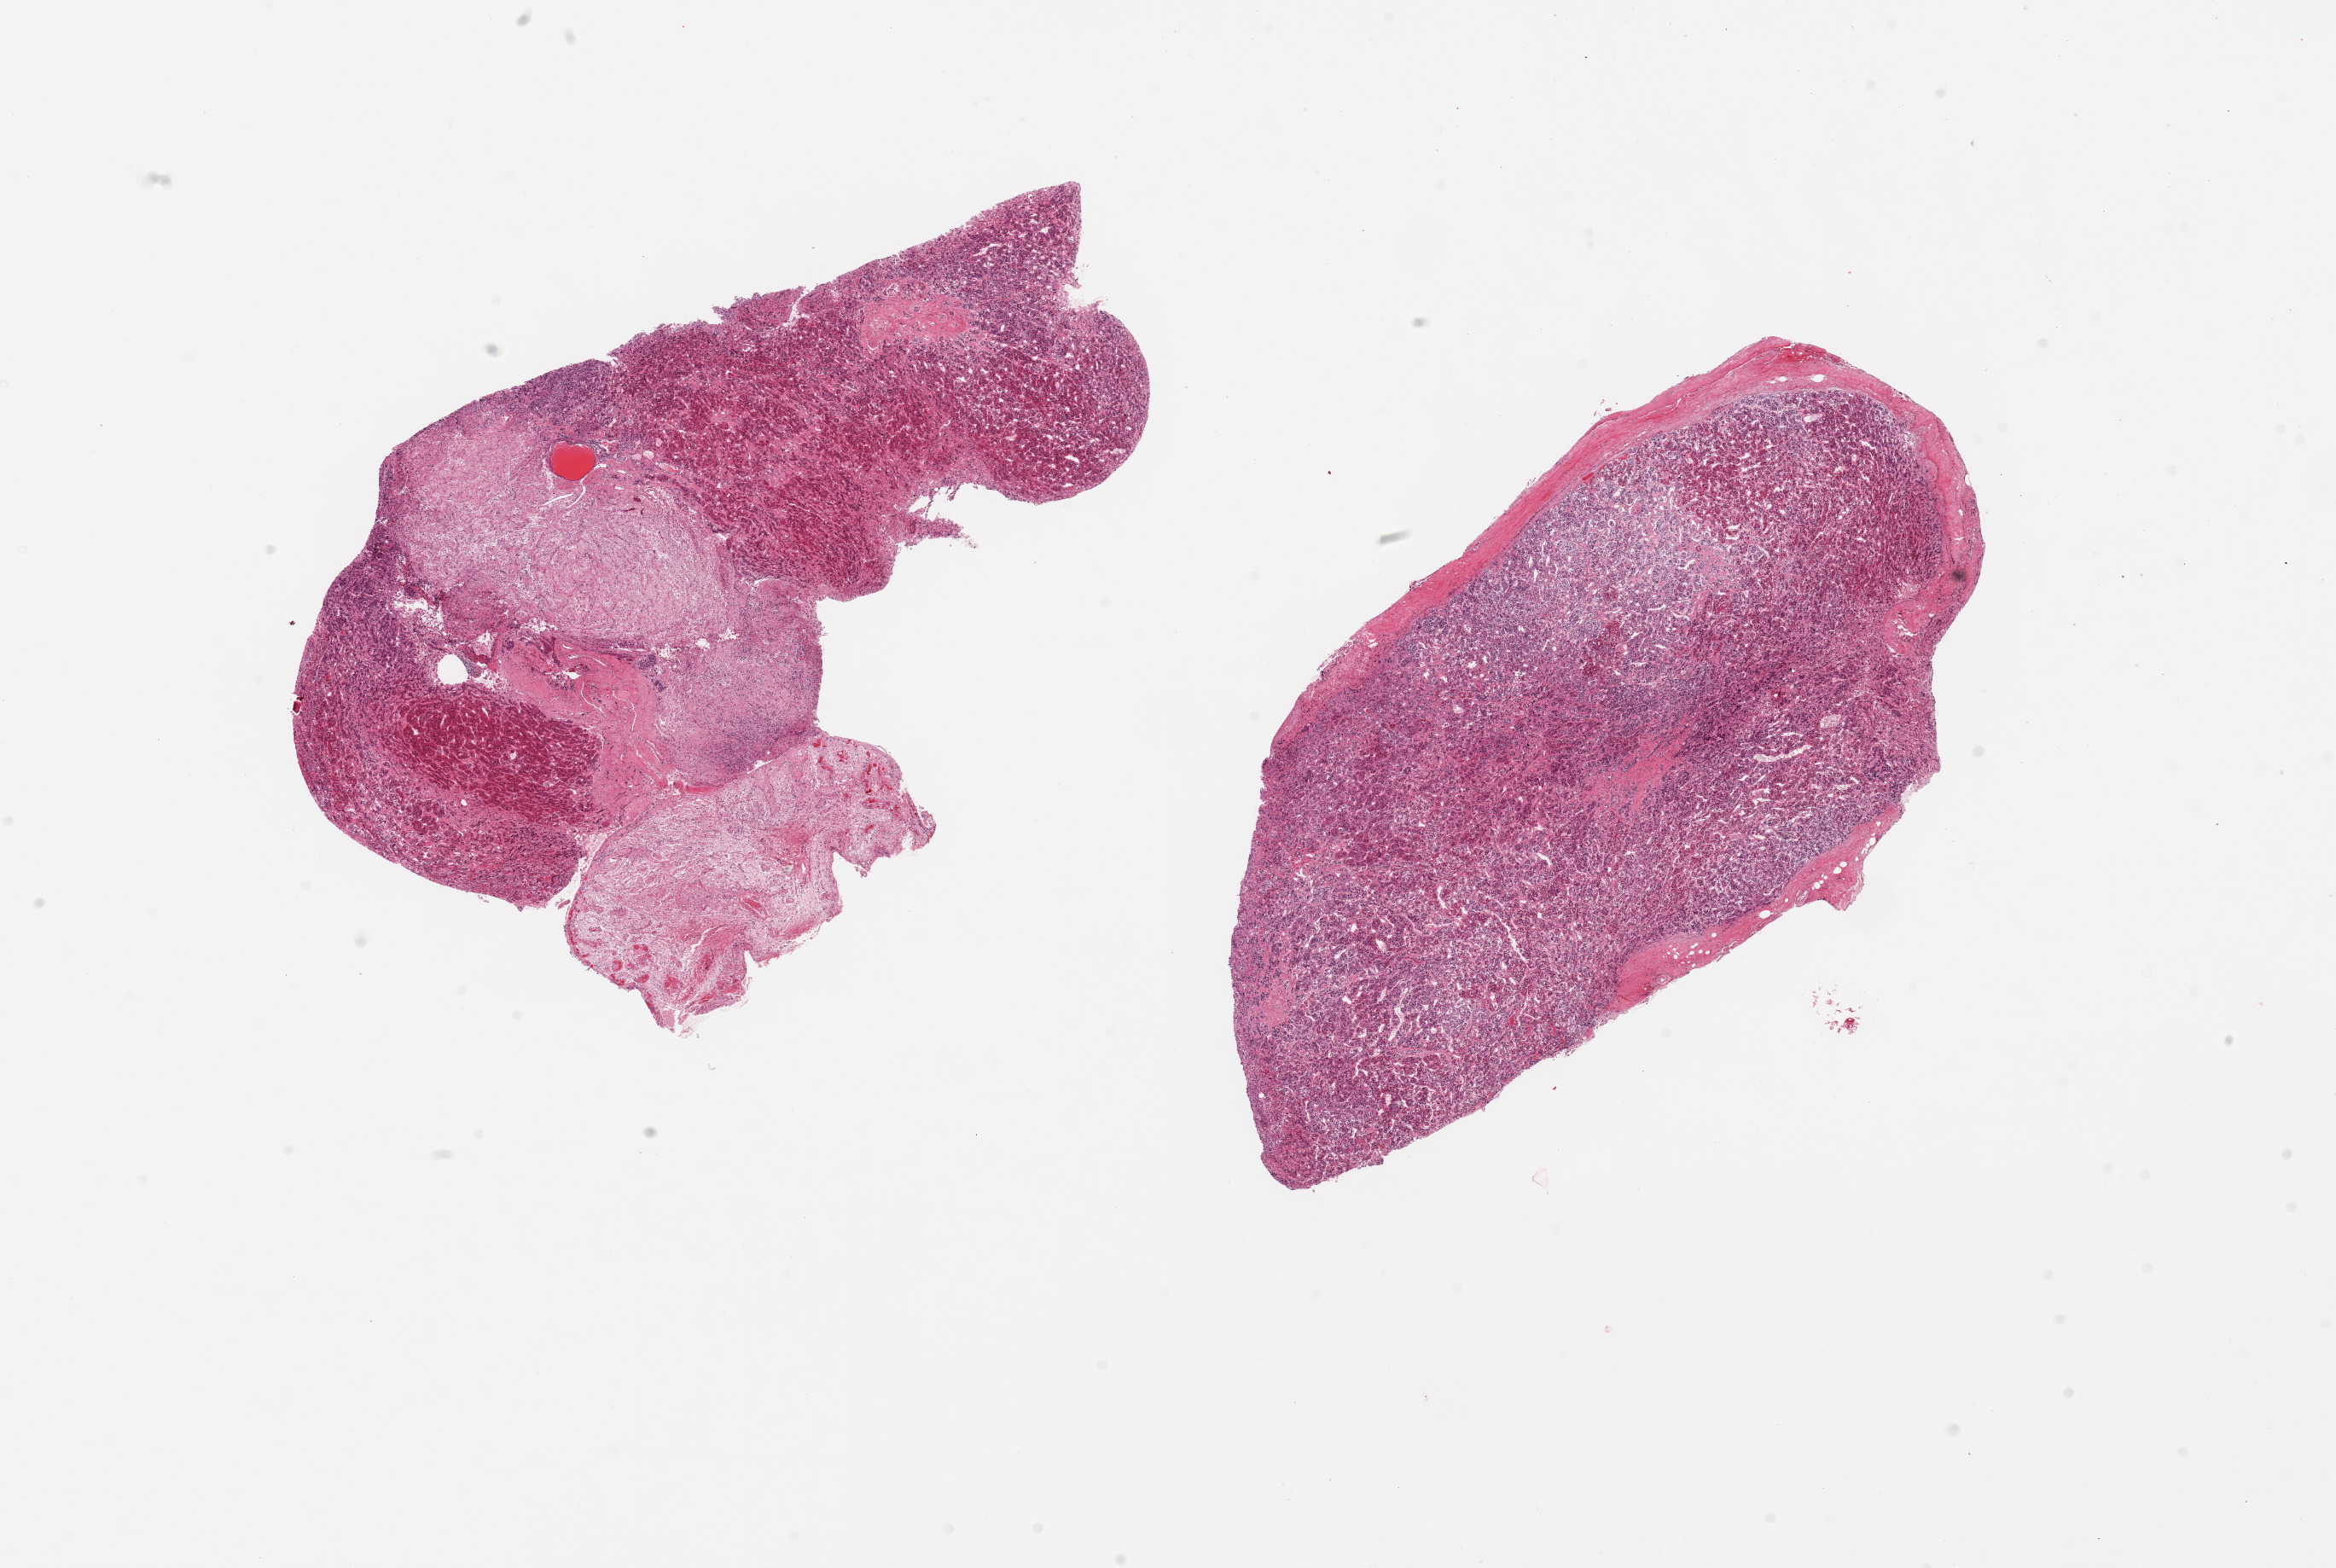
Haematoxylin and eosin whole-slide image — shown as a low-resolution overview of the whole scanned area (about 21.7 x 14.5 mm). PAXgene-fixed paraffin-embedded (PFPE) section. Target tissue: pituitary. Tissue donor sample. Male donor.
- review note (as recorded): 2 pieces, mainly adenohypophysis, ~5x2.5mm portion of neuorhypophysis noted